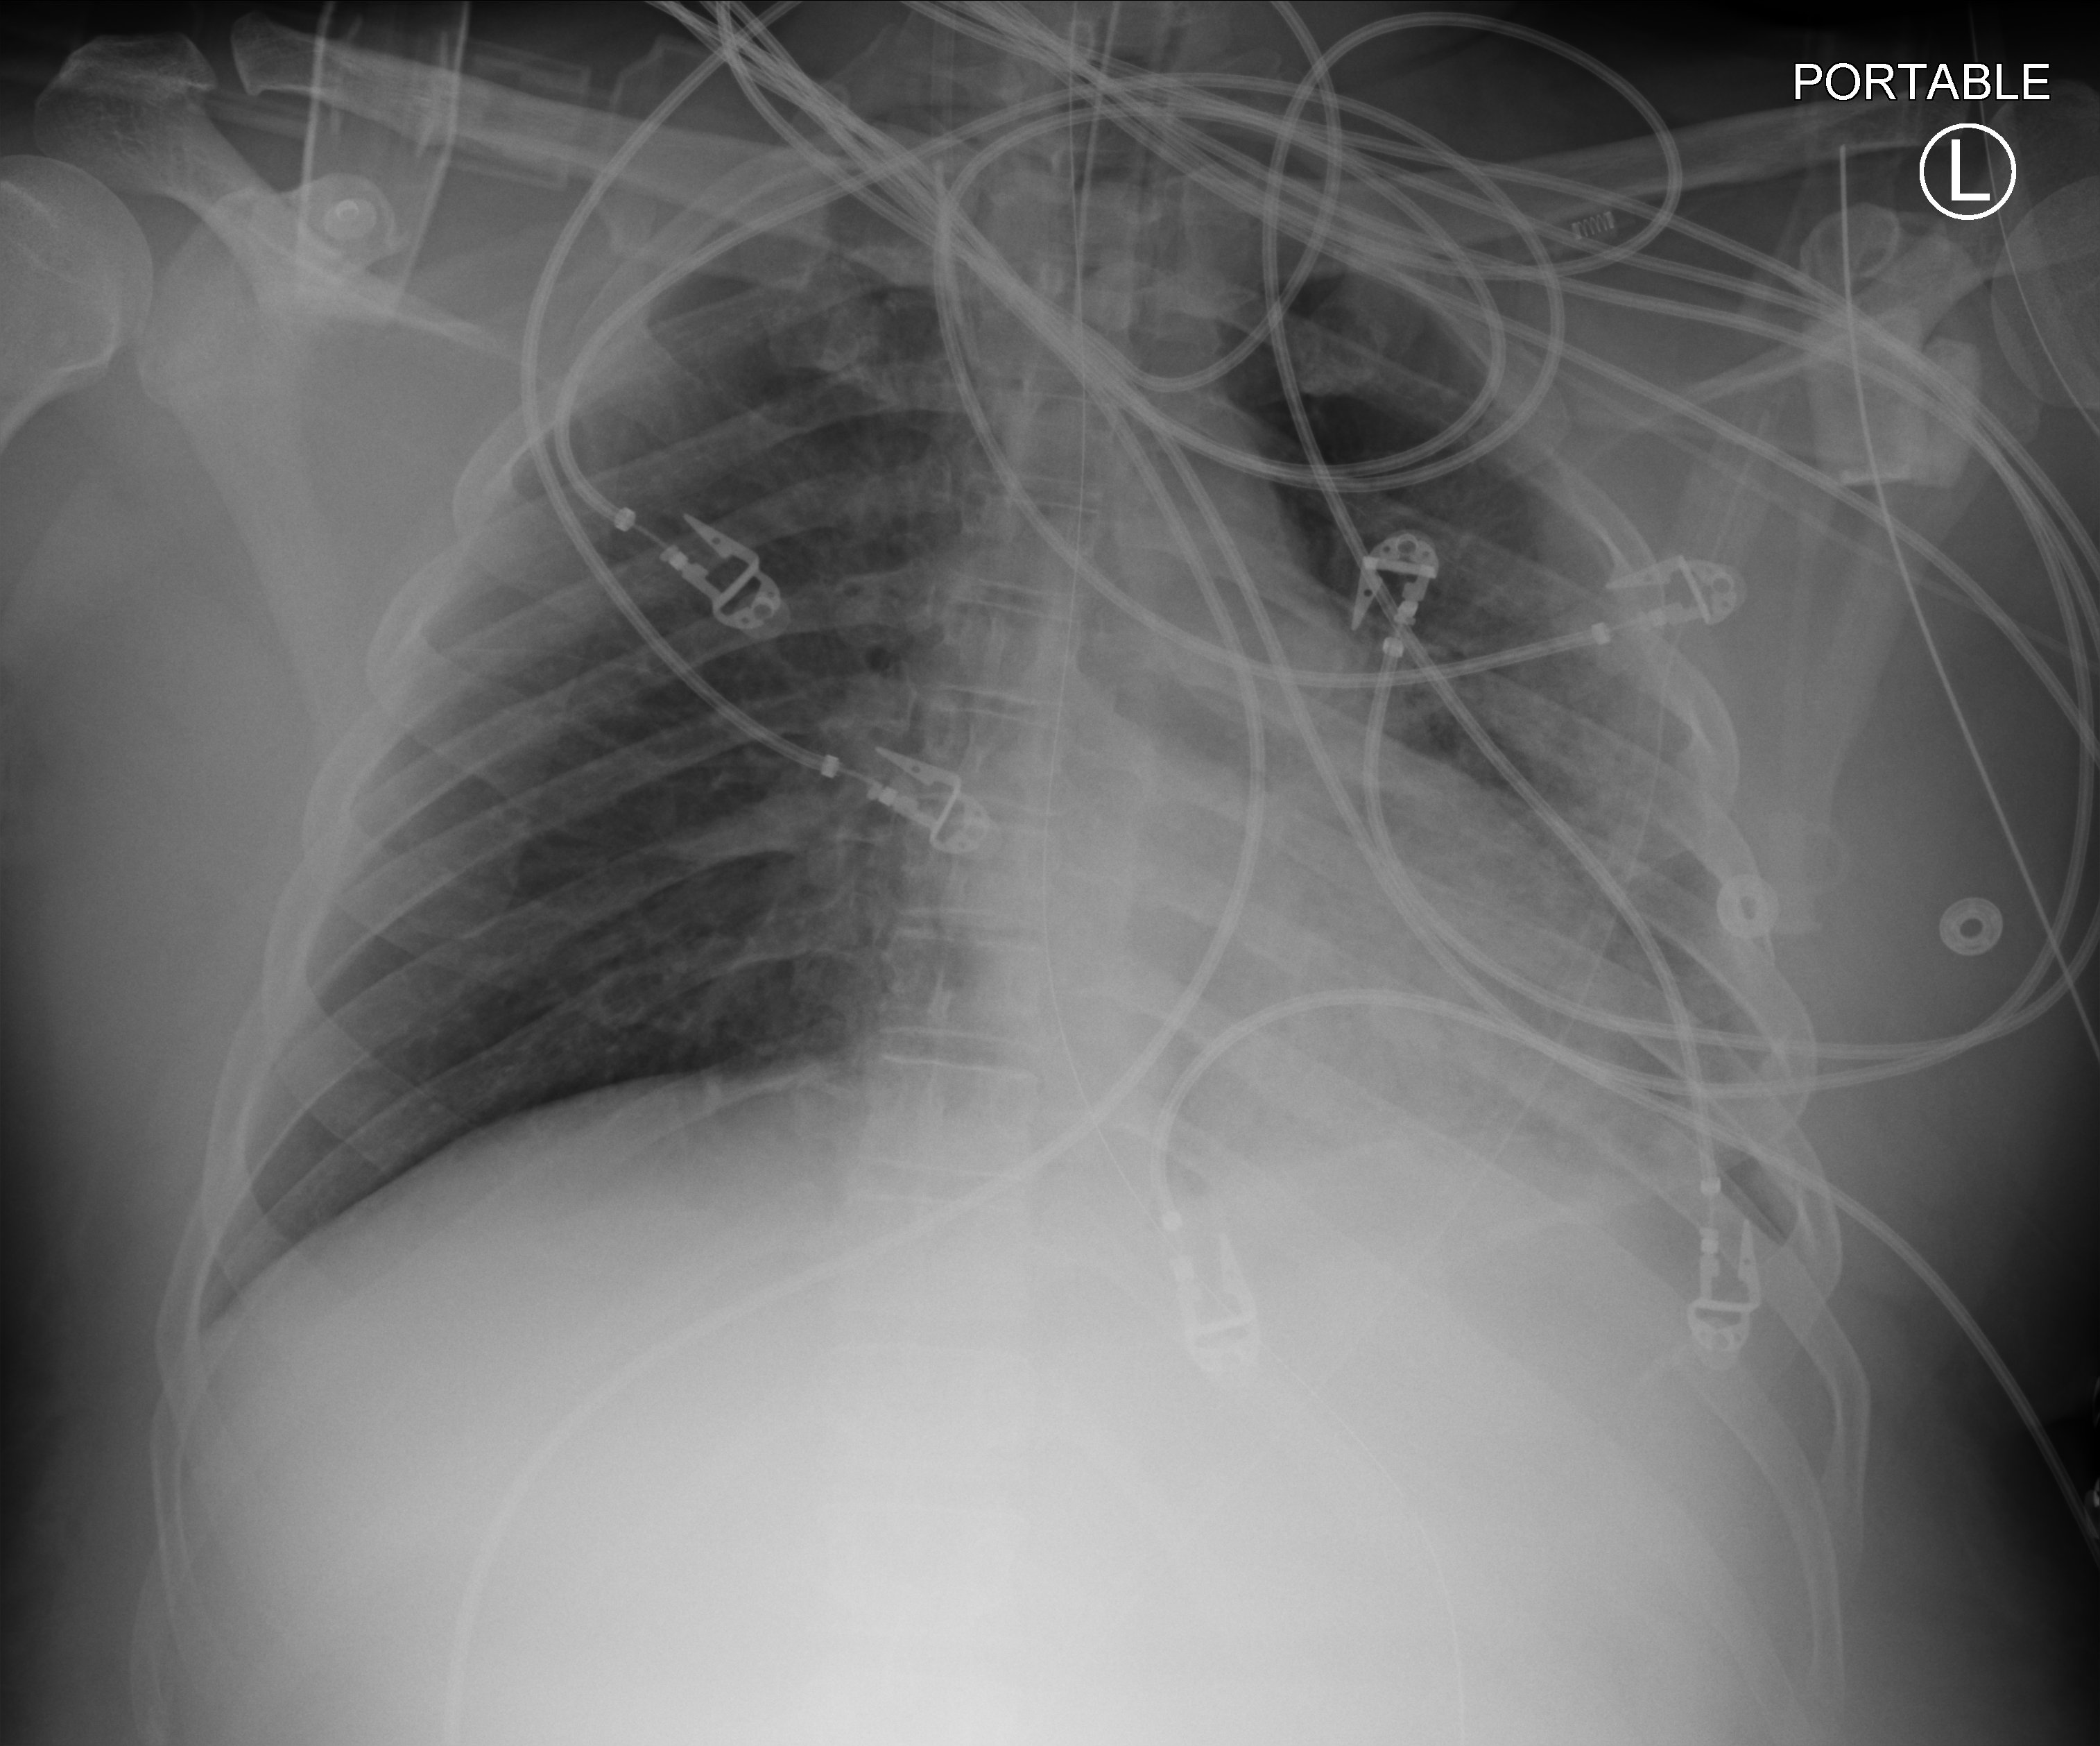
Chest X-ray (portable); anteroposterior (AP) projection. Patient hospitalised with COVID-19, aged 18–59 years.
From the hospital-stay record, not from the radiograph (when in the stay this image was taken is not recorded):
- hypertension (admission record): yes